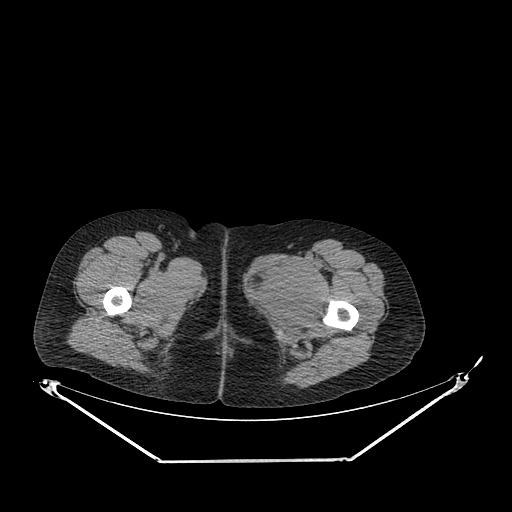
CT of an extremity soft-tissue mass (from a PET/CT study), one axial slice. Slice 253 of 267 in the series (ordered by position). Reconstruction kernel SOFT. Soft-tissue window (W 400 / L 40 HU). 3.75 mm slice thickness. 512 × 512 image matrix. Female patient. From the clinical record (not read from this slice): histological type: pleiomorphic leiomyosarcoma; grade: intermediate; site of the primary tumour: left thigh.
Annotated regions visible in this slice (expert contour drawn on MRI and transferred to this co-registered scan by the dataset authors):
- gross tumour volume including surrounding oedema: bounding box [x1, y1, x2, y2] px = [249, 256, 318, 312]
- gross tumour volume (mass): [249, 256, 318, 312]